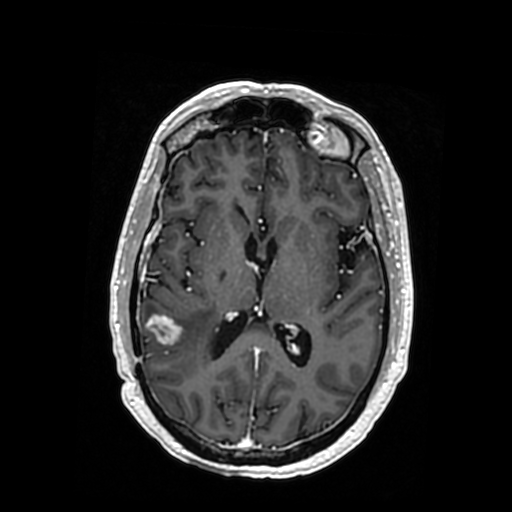
Brain MRI from a brain-tumour surgery series, one axial slice; position 174 of 364 along the scan axis; T1-weighted post-contrast; 512 × 512 image matrix, field of view 260 × 260 mm. Case-level facts recorded for this patient, not image findings: histopathology: Oligodendroglioma; WHO grade: 3; IDH mutation: yes; tumour location: Right Posterior Temporal Inferior Parietal.
Structures marked on this image (expert manual segmentation):
- tumour: bounding box [x1, y1, x2, y2] px = [149, 315, 183, 372]